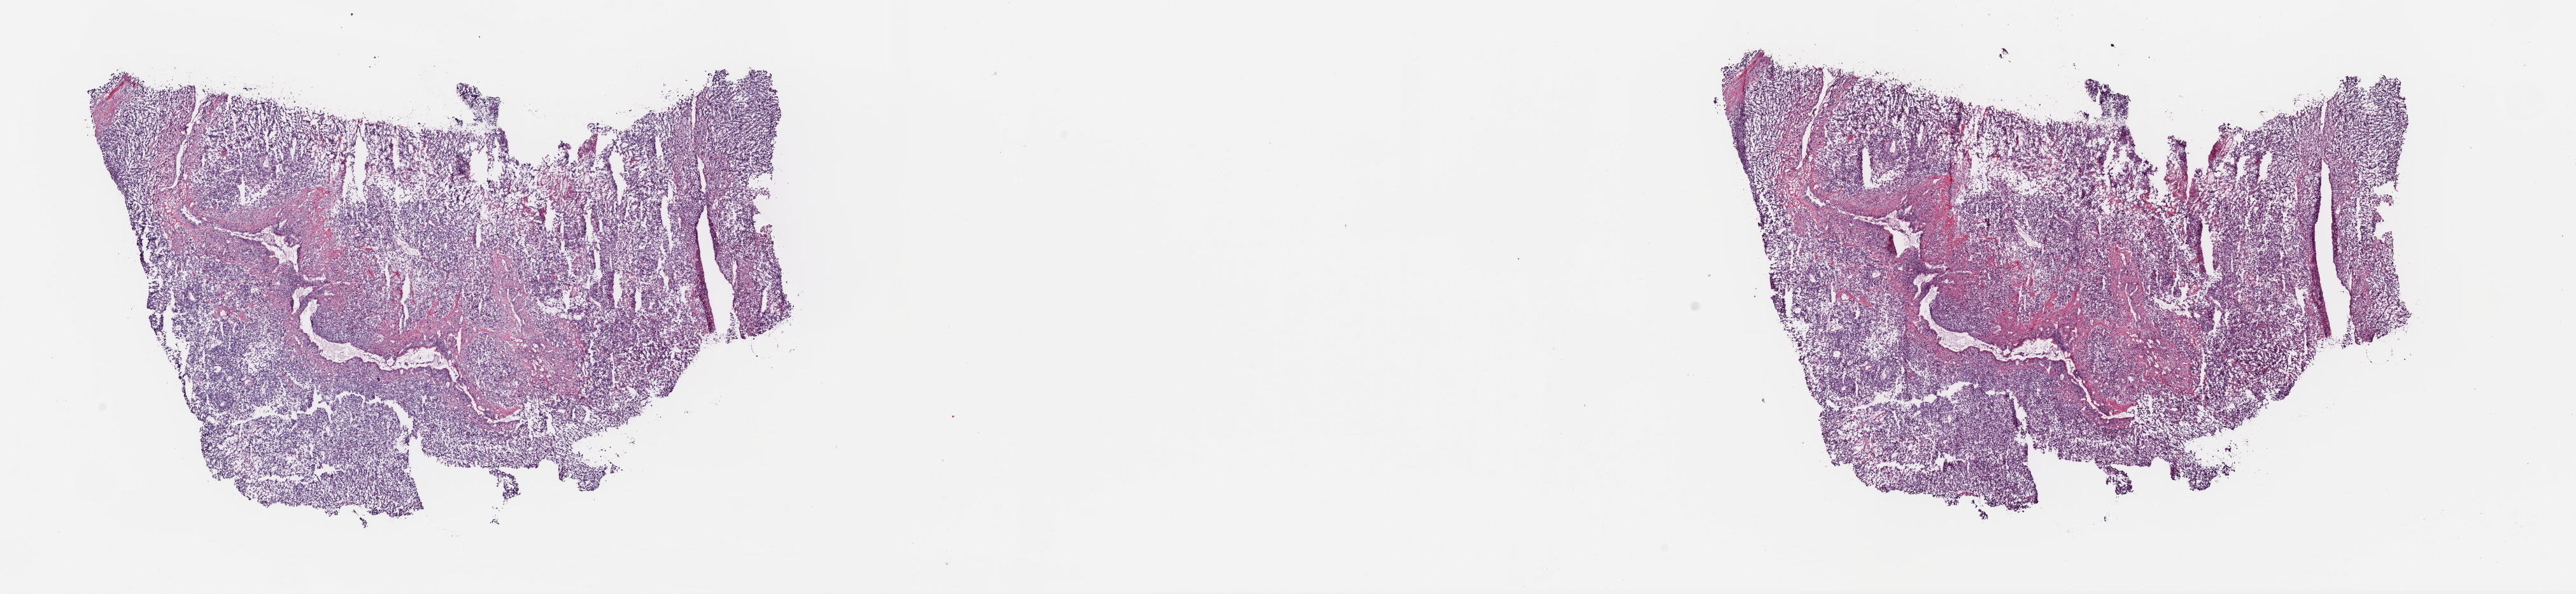
H&E-stained whole-slide image, low-resolution overview of the scanned area, about 32.0 x 7.4 mm (slide scanned at 40x); frozen section; metastatic tumour sample, sampled site: lymph nodes of axilla or arm. Male patient; age at initial diagnosis 30 years. Slide review estimates, as recorded: tumour cells 95%, tumour nuclei 90%, normal cells 0%, stromal cells 0%, necrosis 5%. Inflammatory infiltration, as recorded: lymphocyte infiltration 0%, monocyte infiltration 0%, neutrophil infiltration 0%.
This section: metastatic tumour tissue. Patient diagnosis: Malignant melanoma, NOS.